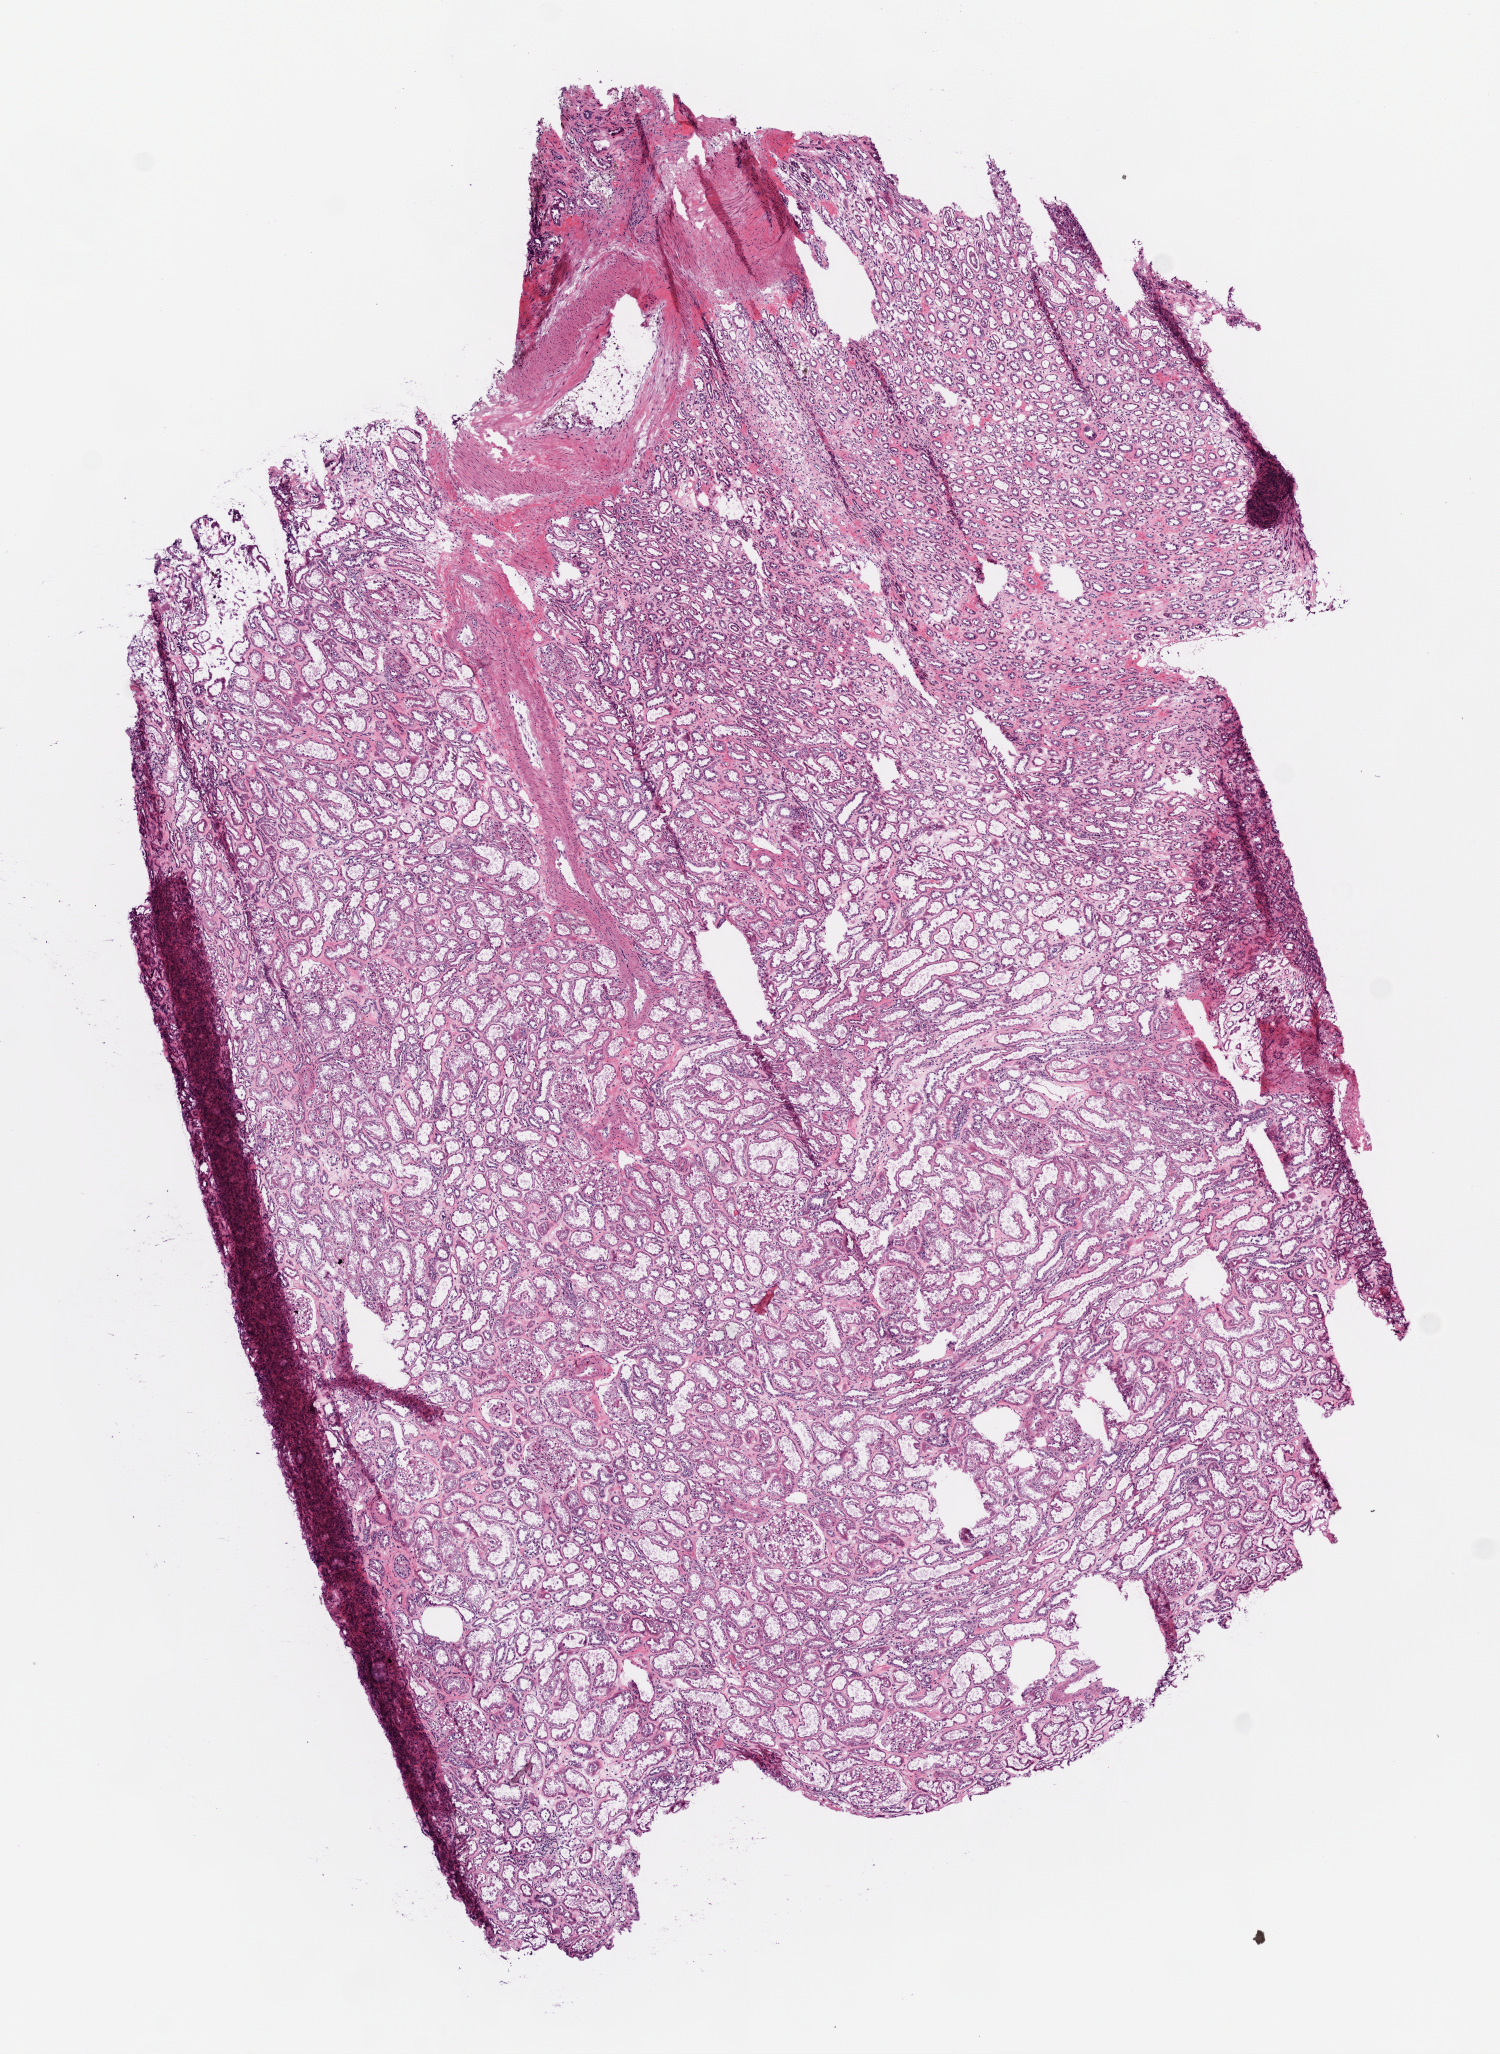
Hematoxylin and eosin (H&E) stained whole-slide image, shown as a low-resolution overview of the whole scanned area (about 6.0 x 8.2 mm, from a 20x scan). Frozen section from the top of the tissue portion. Solid tissue normal (non-tumour tissue) sample from the kidney. Male, age 74 years at initial diagnosis.
* this section: solid tissue normal (non-tumour) sample from the same patient
* patient diagnosis: Clear cell adenocarcinoma, NOS